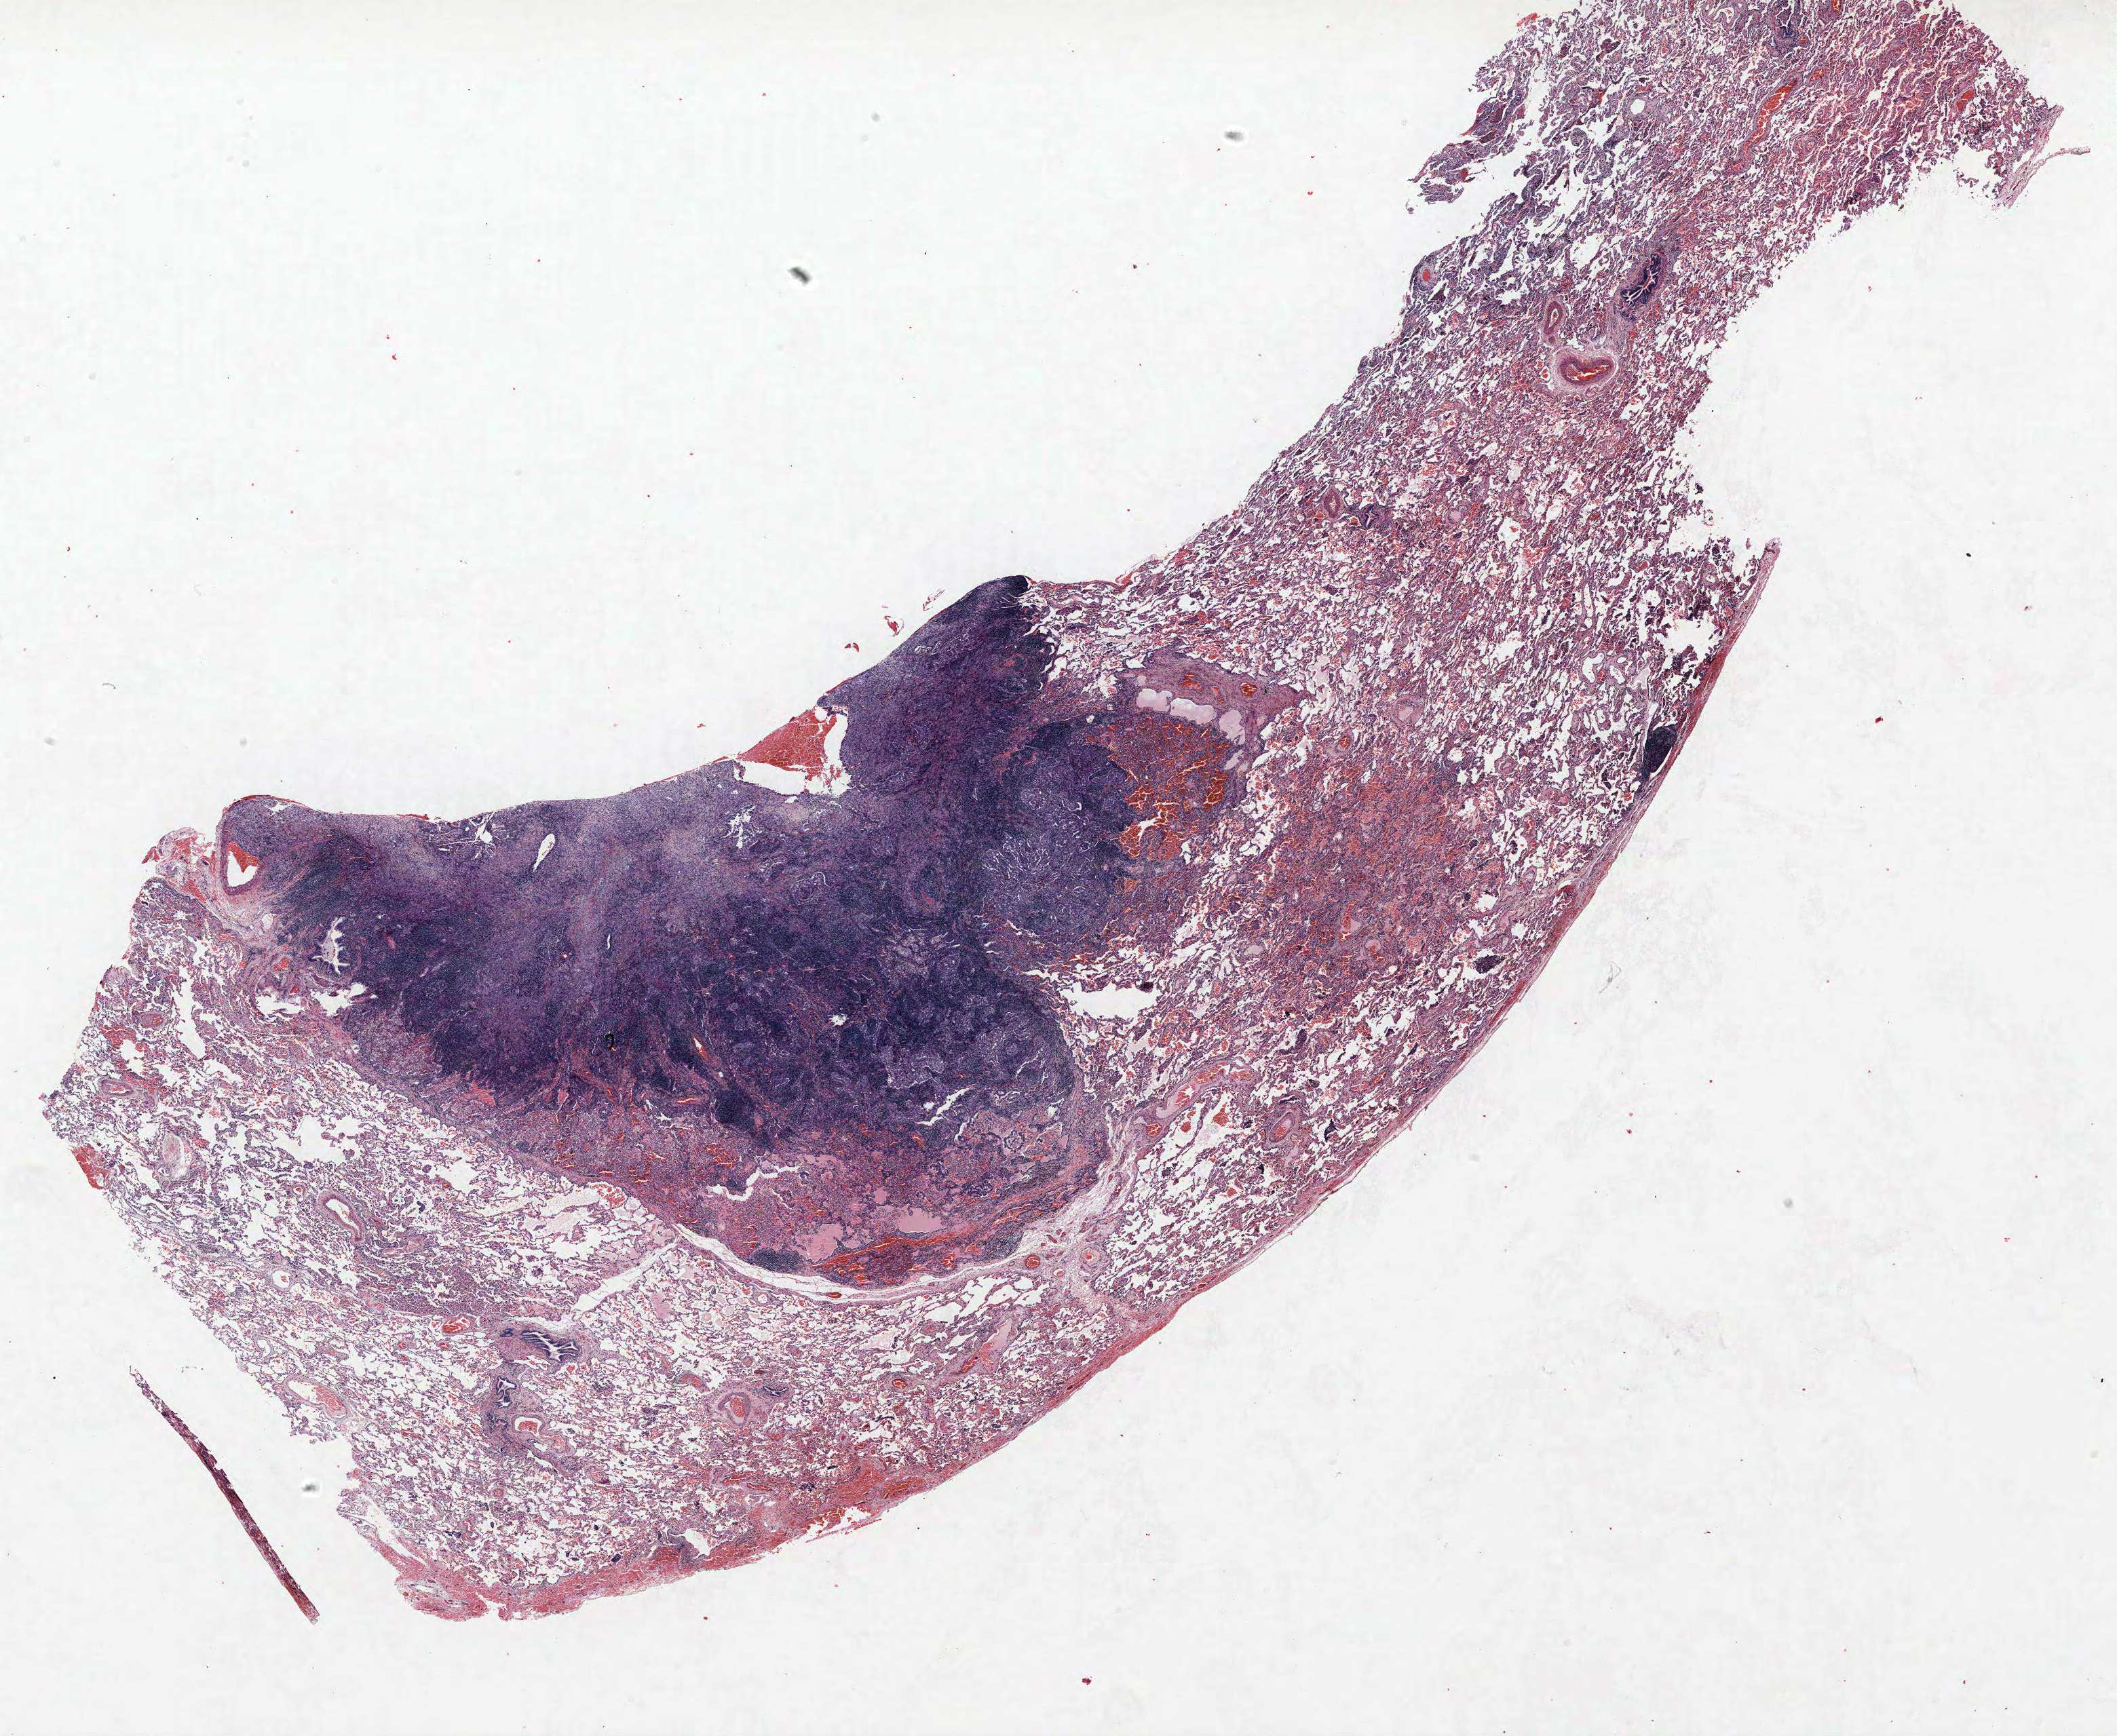
H&E whole-slide image — a low-resolution overview of the entire scanned area, about 25.0 x 20.5 mm, FFPE section, lung. Female, age 55 at enrolment. Grade: well differentiated (G1).
Tumour size (pathology): 11 mm. Stage (AJCC 6th edition): IA. Primary tumour location (clinical record): left lower lobe. Participant's lung-cancer diagnosis: Adenocarcinoma, NOS.